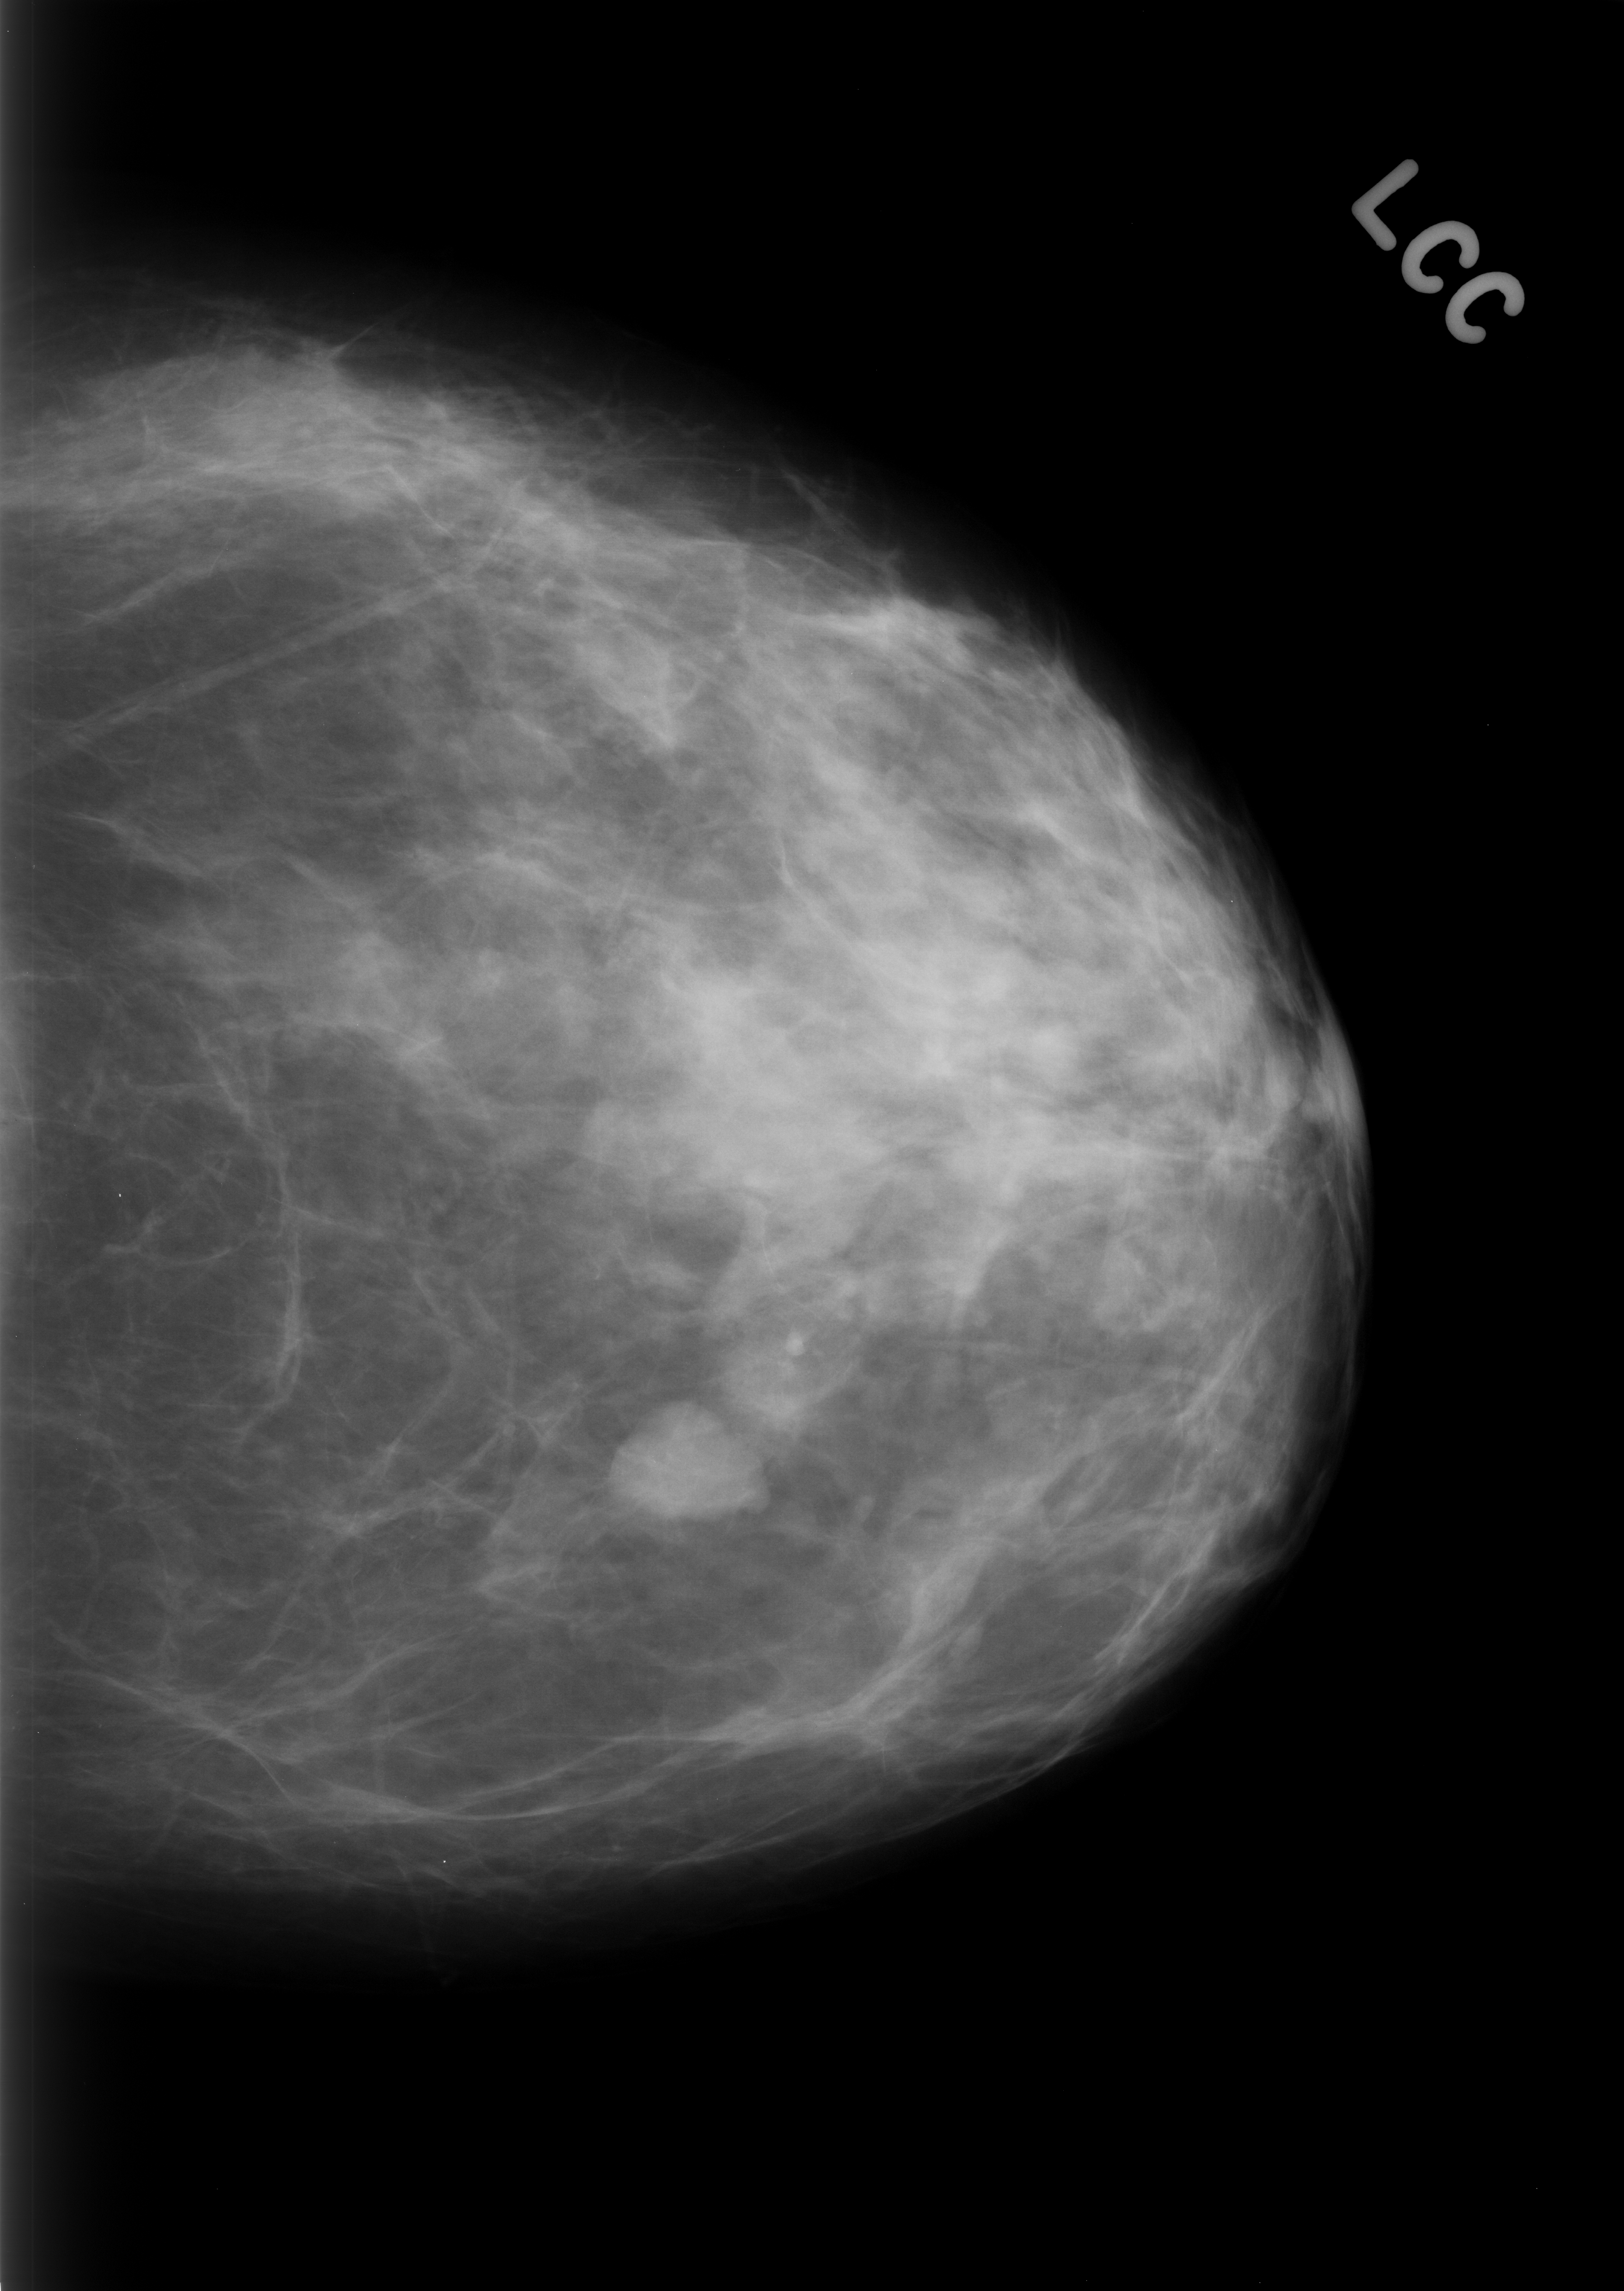
Digitized screen-film mammogram; left breast; CC view; breast composition: scattered fibroglandular densities (BI-RADS density category 2 of 4); 1624 × 2291 image matrix.
Expert-marked regions of interest on this film, with their recorded descriptors:
- mass, shape lobulated, margins circumscribed; BI-RADS assessment category 3; subtlety rating 5 on a 1 (subtle) to 5 (obvious) scale; pathology result (as recorded, not read from the image): benign: box from (x=616, y=1400) to (x=758, y=1522) px